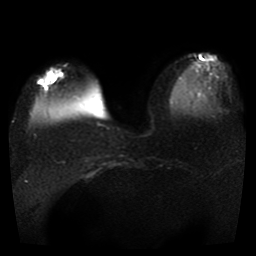
Breast MRI, one axial slice. Slice 9 of 41 in the series (ordered by position). Diffusion-weighted series; image 2 of 4 stored at this slice position (different b-values; order by instance number). 1.5 T. 256 × 256 image matrix, field of view 330 × 330 mm. Female patient.
Structures marked on this image (expert manual segmentation):
- tumour on diffusion-weighted imaging: box from (x=38, y=72) to (x=56, y=85) px